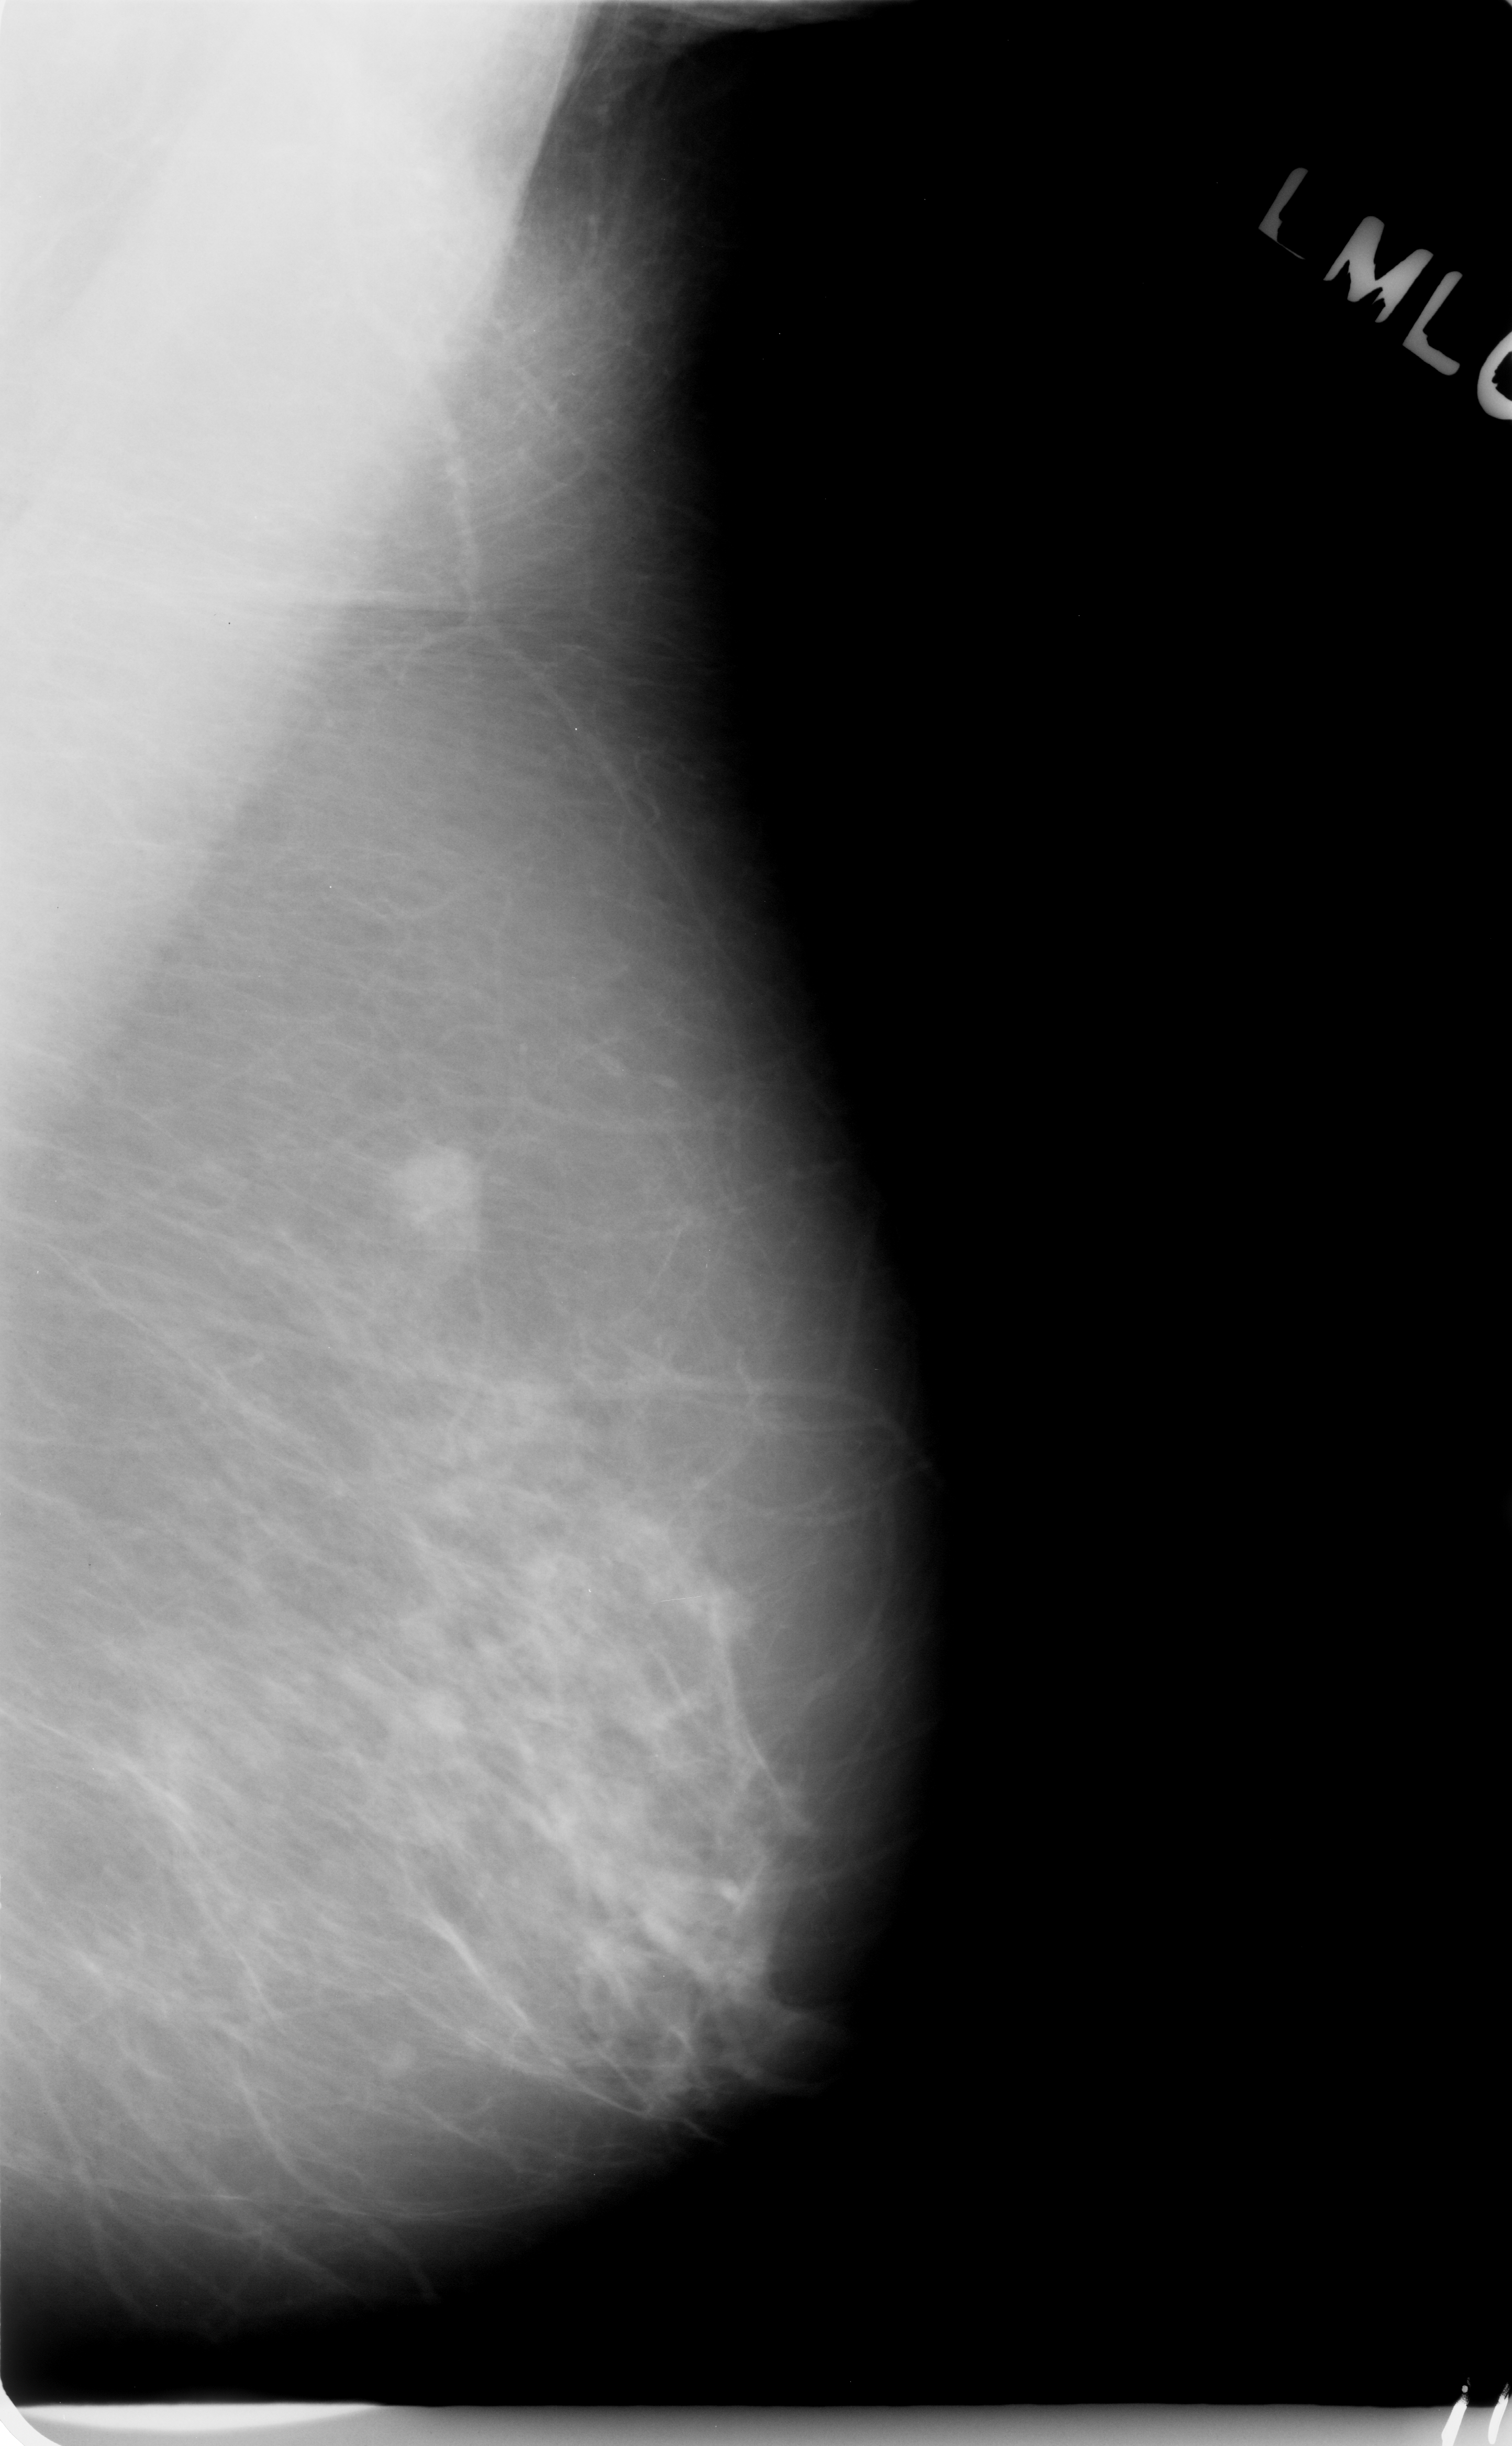
Digitized screen-film mammogram; left breast; MLO view; 1512 × 2446 image matrix.
Expert-marked regions of interest on this image (one box per marked abnormality):
- mass, shape lobulated, margins spiculated; BI-RADS assessment category 5; pathology (as recorded): malignant: bounding box [x1, y1, x2, y2] px = [371, 1129, 504, 1275]